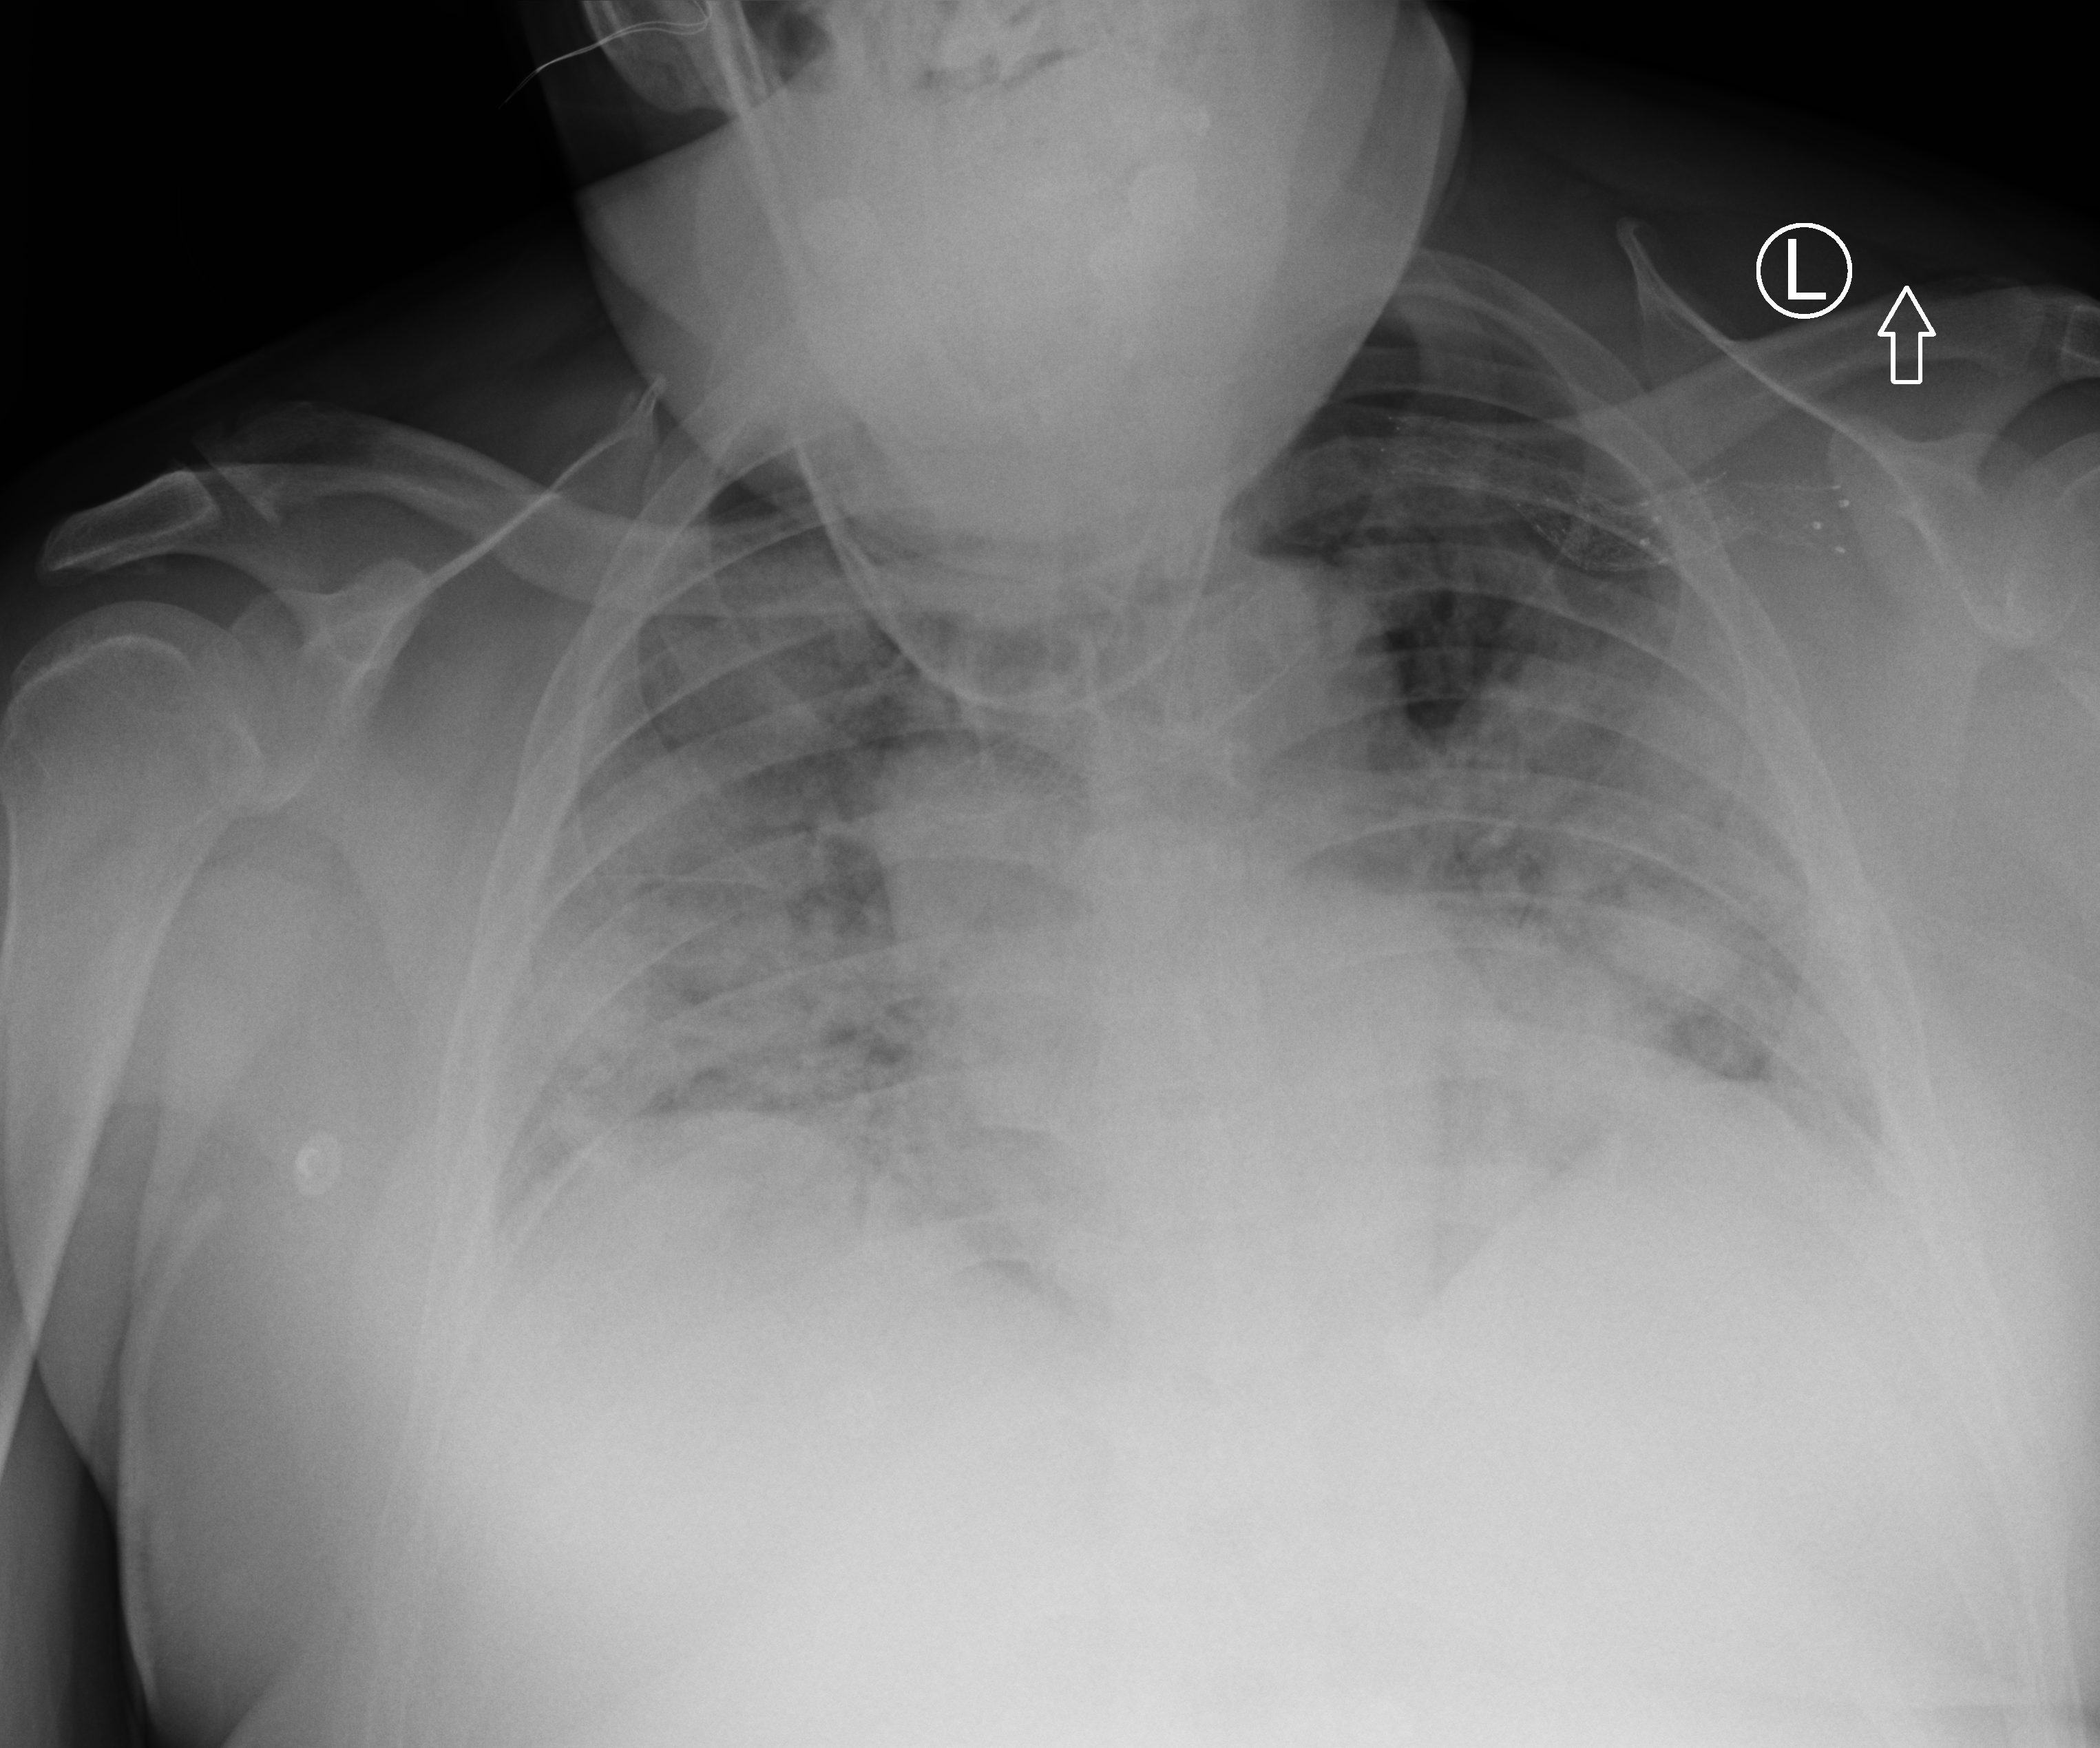
Bedside chest radiograph (computed radiography); anteroposterior (AP) projection. Patient hospitalised with COVID-19; male, aged 18–59 years.
Hospital-stay facts (about this admission, not read from this image; timing relative to this image not recorded): chronic kidney disease (admission record): yes; mechanically ventilated during this hospital stay: yes.